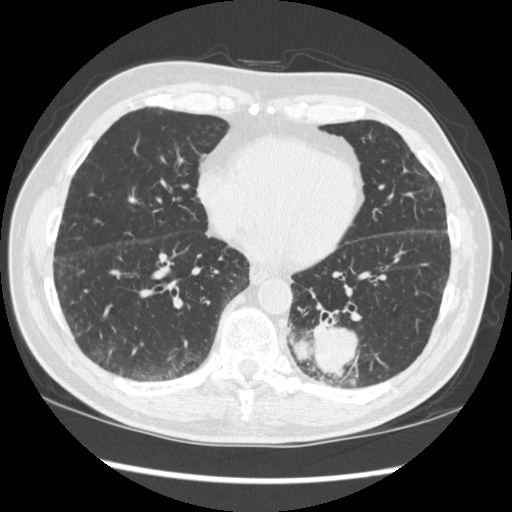
Low-dose screening chest CT, axial slice, baseline annual screen, lung window (W 1500 / L -600 HU). Male participant, aged 72 years at enrolment. Current smoker at enrolment.
Expert-annotated lung lesion, bounding box <273,296,377,384> (left, top, right, bottom; pixels). The screening reader recorded 2 non-calcified nodules or masses ≥4 mm on this exam (left lower lobe, right middle lobe); which of them this box marks is not recorded. Official screen result: positive, change unspecified: nodule(s) >= 4 mm or enlarging nodule(s), mass(es), or other non-specific abnormalities suspicious for lung cancer. Participant outcome: lung cancer diagnosed 37 days after this screen — squamous cell carcinoma, NOS, left lower lobe, stage IIIA (AJCC 6th edition), 60 mm at pathology.